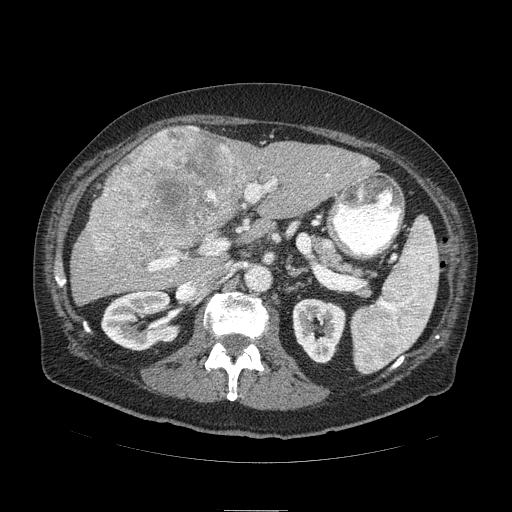
Contrast-enhanced abdominal CT (liver protocol), one axial slice; slice 46 of 103 in the series (ordered by position); 120 kVp; soft-tissue window (W 400 / L 40 HU); 512 × 512 image matrix, field of view 440 × 440 mm. Case-level facts recorded for this patient, not image findings: diagnosis: hepatocellular carcinoma (patient treated with transarterial chemoembolisation; whether this scan precedes or follows treatment is not stated here); TNM stage (as recorded): Stage-IIIA; Child-Pugh class: B.
Annotated regions visible in this slice (semi-automatic segmentation, software-assisted and operator-edited):
- liver parenchyma outside the tumour (the mass and vessels are separate outlines, so this box may not span the whole liver): box from (x=70, y=126) to (x=376, y=304) px
- mass: (x=88, y=128)–(x=255, y=264)
- liver vessels: (x=149, y=174)–(x=329, y=272)